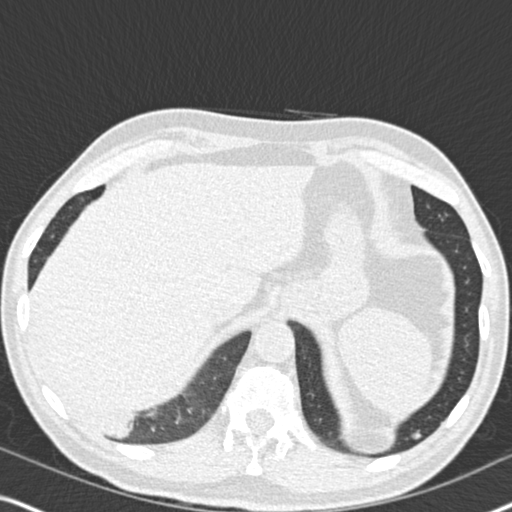
Low-dose screening chest CT, one axial slice; position 45 of 182 along the scan axis; reconstruction kernel B30f; lung window (W 1500 / L -600 HU); 2 mm slice thickness; 512 × 512 image matrix, field of view 330 × 330 mm.
Annotated regions visible in this slice (manually delineated by an expert):
- lesion 1 (tumor, lower lobe of right lung): bounding box (x1, y1, x2, y2) in pixels: (82, 410, 135, 435)